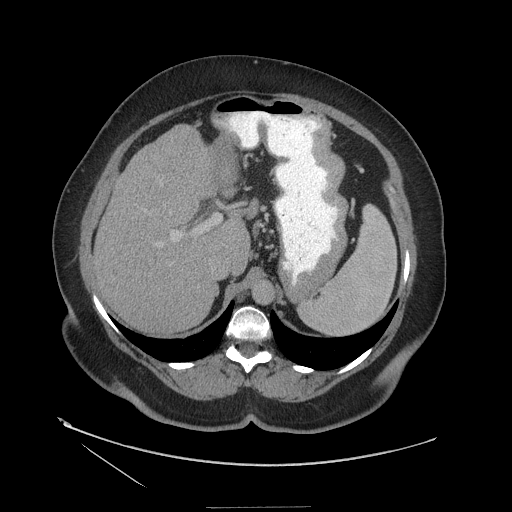
Contrast-enhanced abdominal CT (liver protocol), one axial slice; position 79 of 127 along the scan axis; reconstruction kernel STANDARD; 140 kVp; soft-tissue window (W 400 / L 40 HU); 2.5 mm slice thickness; 512 × 512 image matrix. From the clinical record (not read from this slice): diagnosis: hepatocellular carcinoma (patient treated with transarterial chemoembolisation; whether this scan precedes or follows treatment is not stated here); TNM stage (as recorded): Stage-II.
Outlined on this slice (semi-automatically segmented with operator editing):
- liver parenchyma outside the tumour (the mass and vessels are separate outlines, so this box may not span the whole liver): box from (x=94, y=114) to (x=268, y=334) px
- liver vessels: (x=175, y=112)–(x=268, y=236)